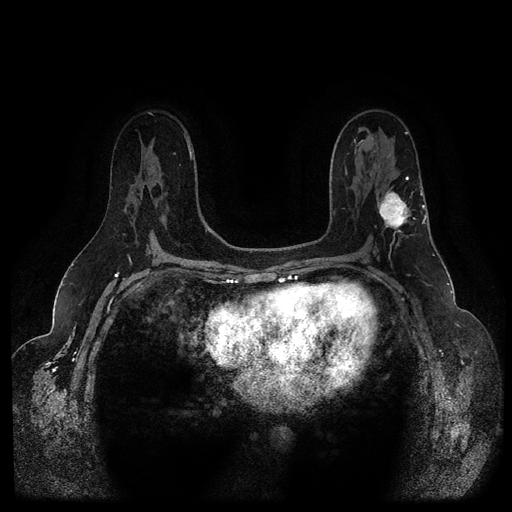
Breast MRI (dynamic contrast-enhanced, multi-phase), one axial slice. Slice 61 of 116 in the series (ordered by position). Dynamic contrast-enhanced series, time point 2 of 5 at this slice position (early post-contrast). 1.5 T. TE 2.6 ms, TR 5.3 ms. 2 mm slice thickness. 512 × 512 image matrix. Patient: female, 54 years.
Outlined on this slice (semi-automatic segmentation, software-assisted and operator-edited):
- breast lesion (labelled 'tumour' in the annotation; benign lesions carry a separate 'benign' label): bounding box [x1, y1, x2, y2] px = [376, 186, 413, 231]